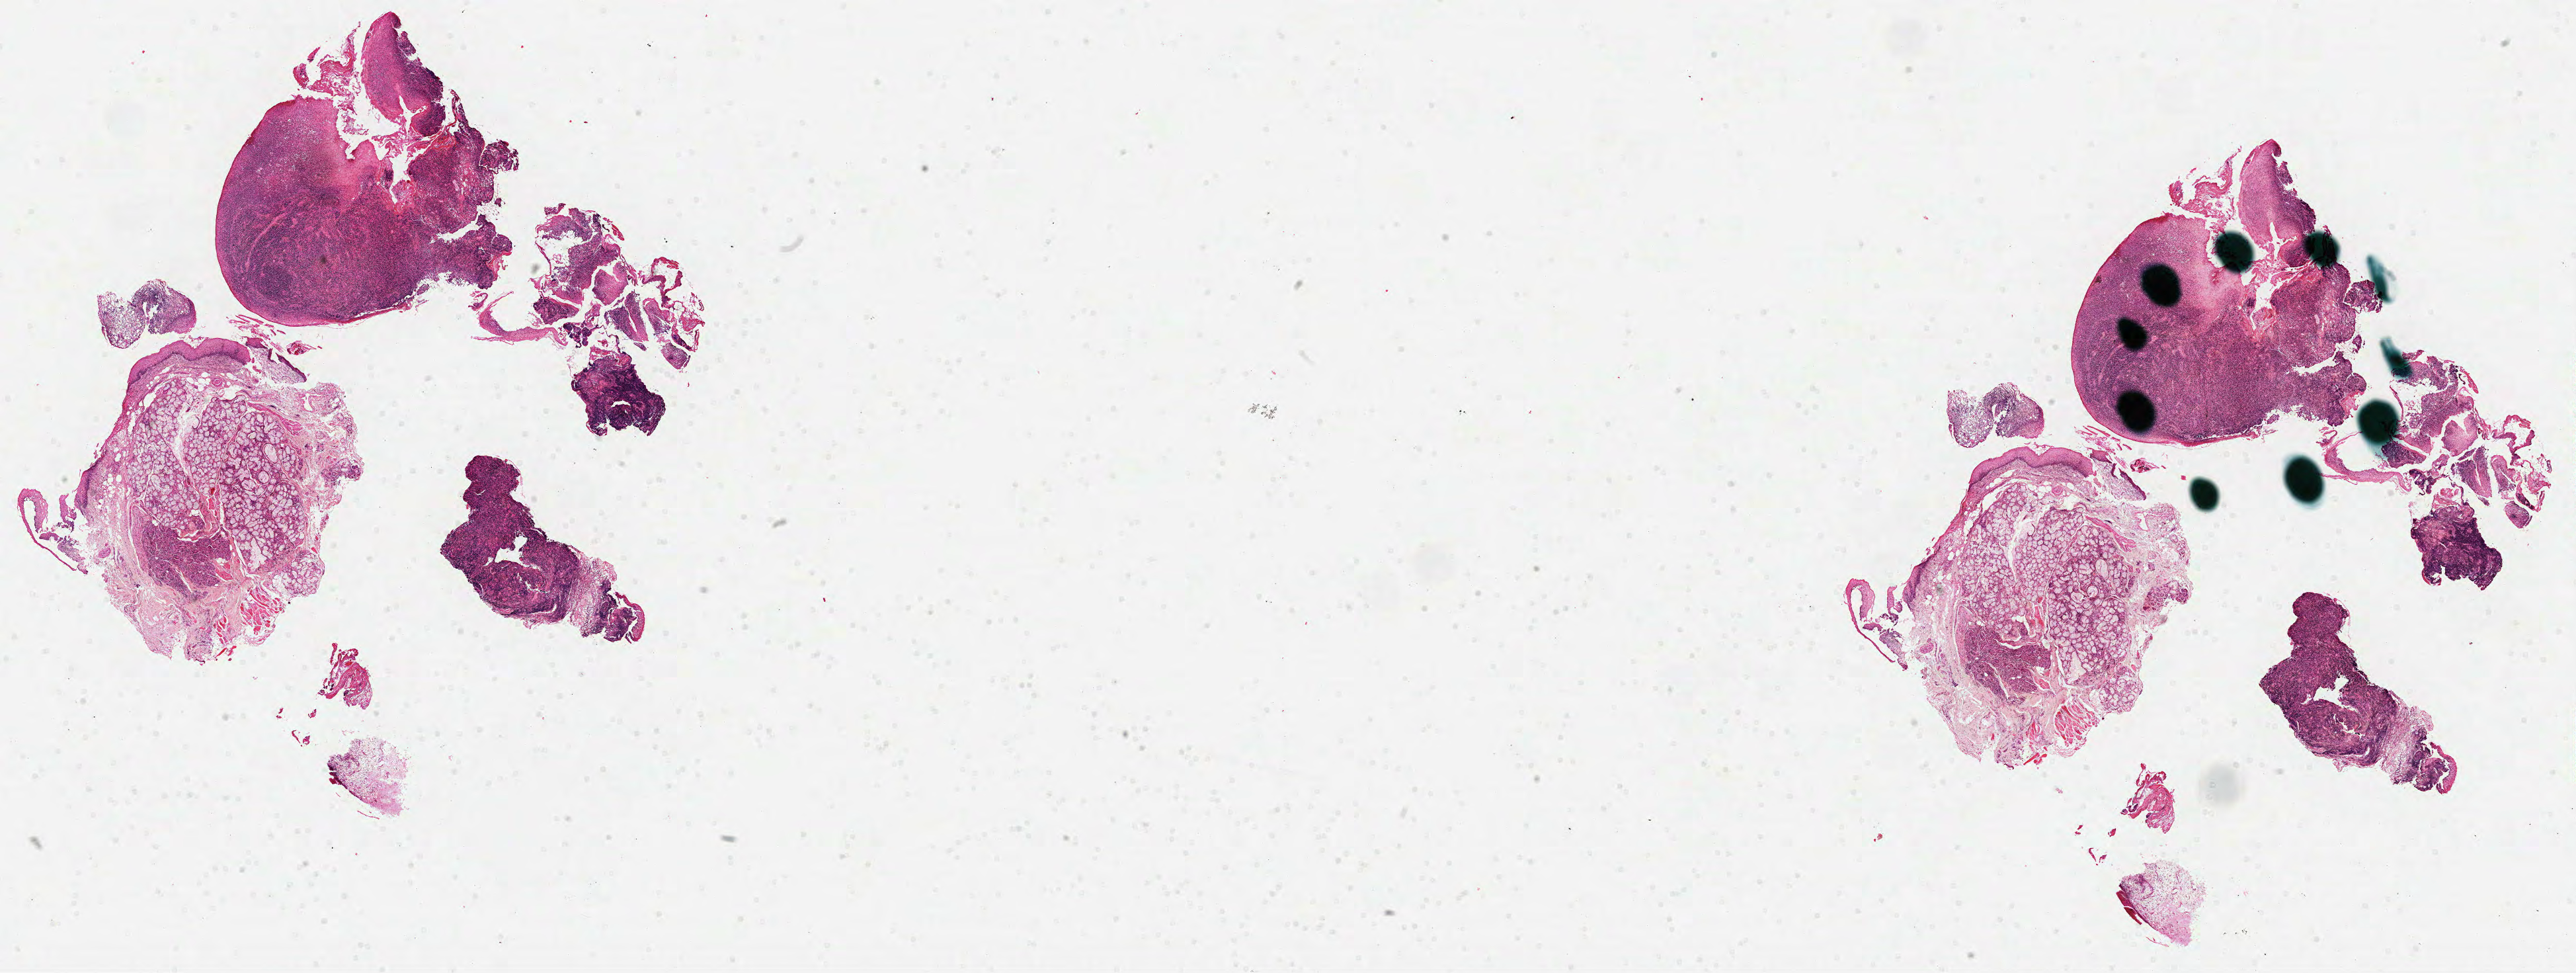
Whole-slide histology image, H&E — low-resolution overview of the scanned area, about 31.4 x 11.9 mm, formalin-fixed paraffin-embedded (FFPE) diagnostic section, primary tumour sample from the head and neck. Patient: male, age at initial diagnosis 56 years.
Histologic diagnosis: Squamous cell carcinoma, NOS.